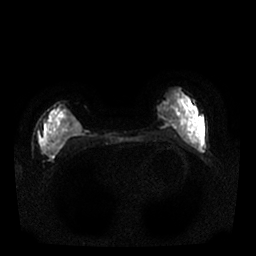
Breast MRI, one axial slice; position 9 of 25 along the scan axis; diffusion-weighted series; image 2 of 4 stored at this slice position (different b-values; order by instance number); 1.5 T; 256 × 256 image matrix, field of view 340 × 340 mm. Female patient.
Annotated regions visible in this slice (expert manual segmentation):
- tumour on diffusion-weighted imaging: bounding box [x1, y1, x2, y2] px = [39, 107, 65, 157]